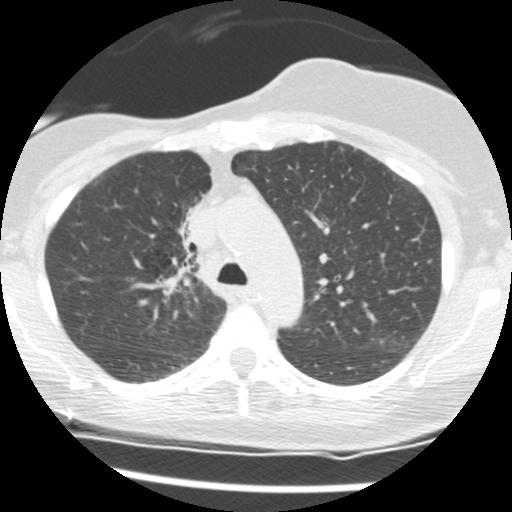
Axial slice from a low-dose chest CT screening exam; second annual screen; lung window (W 1500 / L -600 HU); 2.5 mm slice thickness; standard (soft-tissue) reconstruction kernel (STANDARD); 512 × 512 image matrix. Female participant, aged 56 years at enrolment. Current smoker at enrolment.
• Expert reader's lesion annotation, bounding box <154,195,213,275> (left, top, right, bottom; pixels).
• The screening reader recorded 2 non-calcified nodules or masses ≥4 mm on this exam (right middle lobe, right lower lobe); which of them this box marks is not recorded.